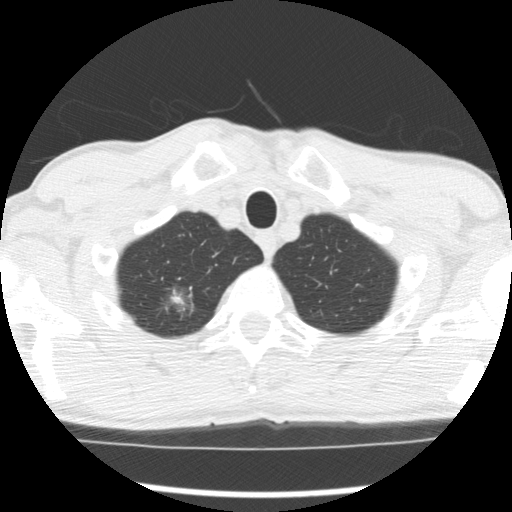
Chest CT (low-dose screening protocol), one axial image. First (baseline) screen. Lung window (W 1500 / L -600 HU). 2.5 mm slice thickness. Standard (soft-tissue) reconstruction kernel (STANDARD). Slice 26 of 277 in the series. 512 × 512 image matrix. Male, age 66 years at enrolment.
Lesion marked by an expert reader, bounding box (x1, y1, x2, y2) in pixels: (153, 283, 202, 329). The screening reader recorded 4 non-calcified nodules or masses ≥4 mm on this exam (right upper lobe, right upper lobe, right upper lobe, left lower lobe); which of them this box marks is not recorded. Official screen result: positive, change unspecified: nodule(s) >= 4 mm or enlarging nodule(s), mass(es), or other non-specific abnormalities suspicious for lung cancer. Later outcome: lung cancer diagnosed 503 days after this screen — adenocarcinoma, NOS, right upper lobe, undifferentiated (G4), stage IA (AJCC 6th edition), 20 mm at pathology.